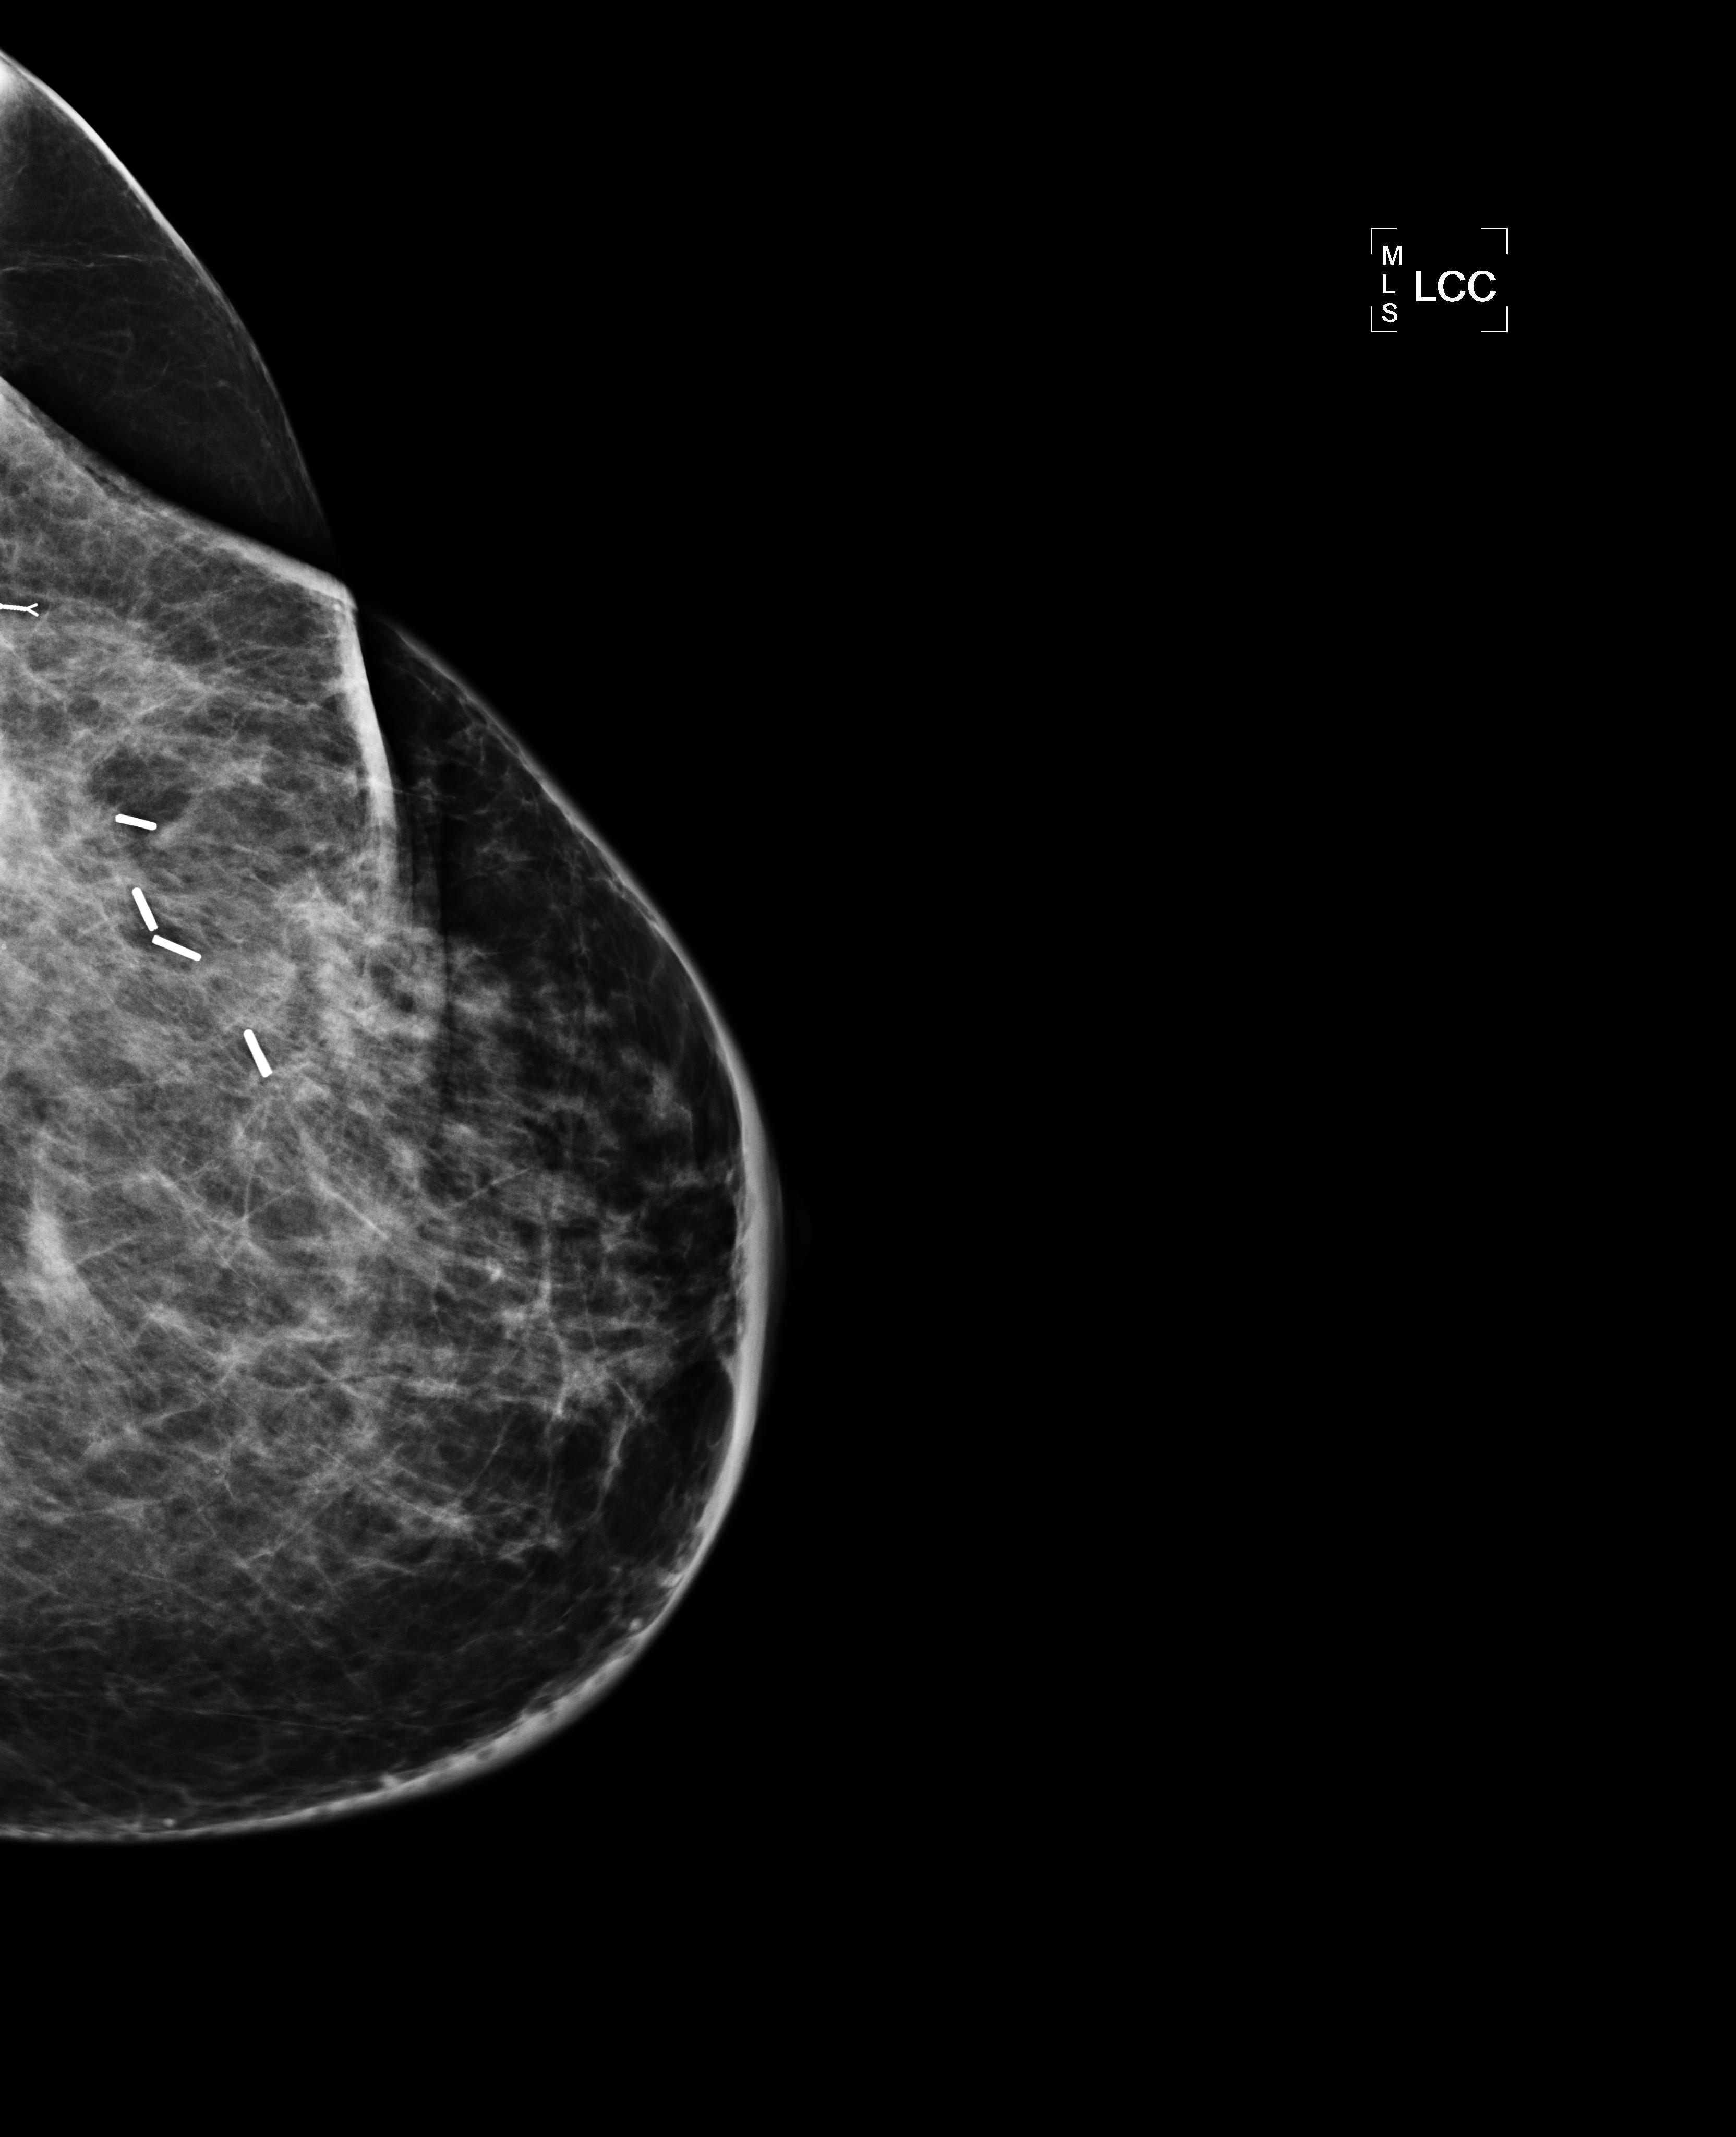
Mammogram, left breast, CC view; patient in her 50s.
Pathology recorded for this patient (not read from this image): pathology diagnosis: Invasive ductal CA (left breast); receptor status (as recorded): ER pos, PR pos (weak), HER2 neg; Ki-67 (as recorded): intermed prolif; pathology report notes: re-bx [date] was scar tissue from RT rx.